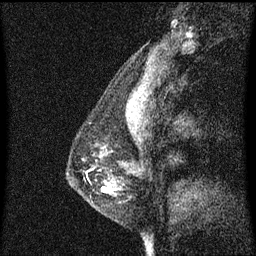
Breast MRI (dynamic contrast-enhanced), one sagittal slice. Slice 18 of 60 in the series (ordered by position). Dynamic contrast-enhanced series, image 2 of 3 at this slice position (ordered by acquisition). 1.5 T. TE 4.2 ms, TR 8.4 ms. 256 × 256 image matrix. Female patient, age 41 years. From the clinical record (not read from this slice): setting: breast cancer imaged before/during neoadjuvant chemotherapy; receptor status: triple-negative.
Annotated regions visible in this slice (semi-automatic segmentation, software-assisted and operator-edited):
- analysis volume of interest (the breast-tissue region the enhancement analysis was run in; not a lesion): bounding box <68,146,135,209> (left, top, right, bottom; pixels)
- tumour enhancement mask (voxels above the 70 % enhancement threshold inside the analysis volume of interest): <102,188,107,193>